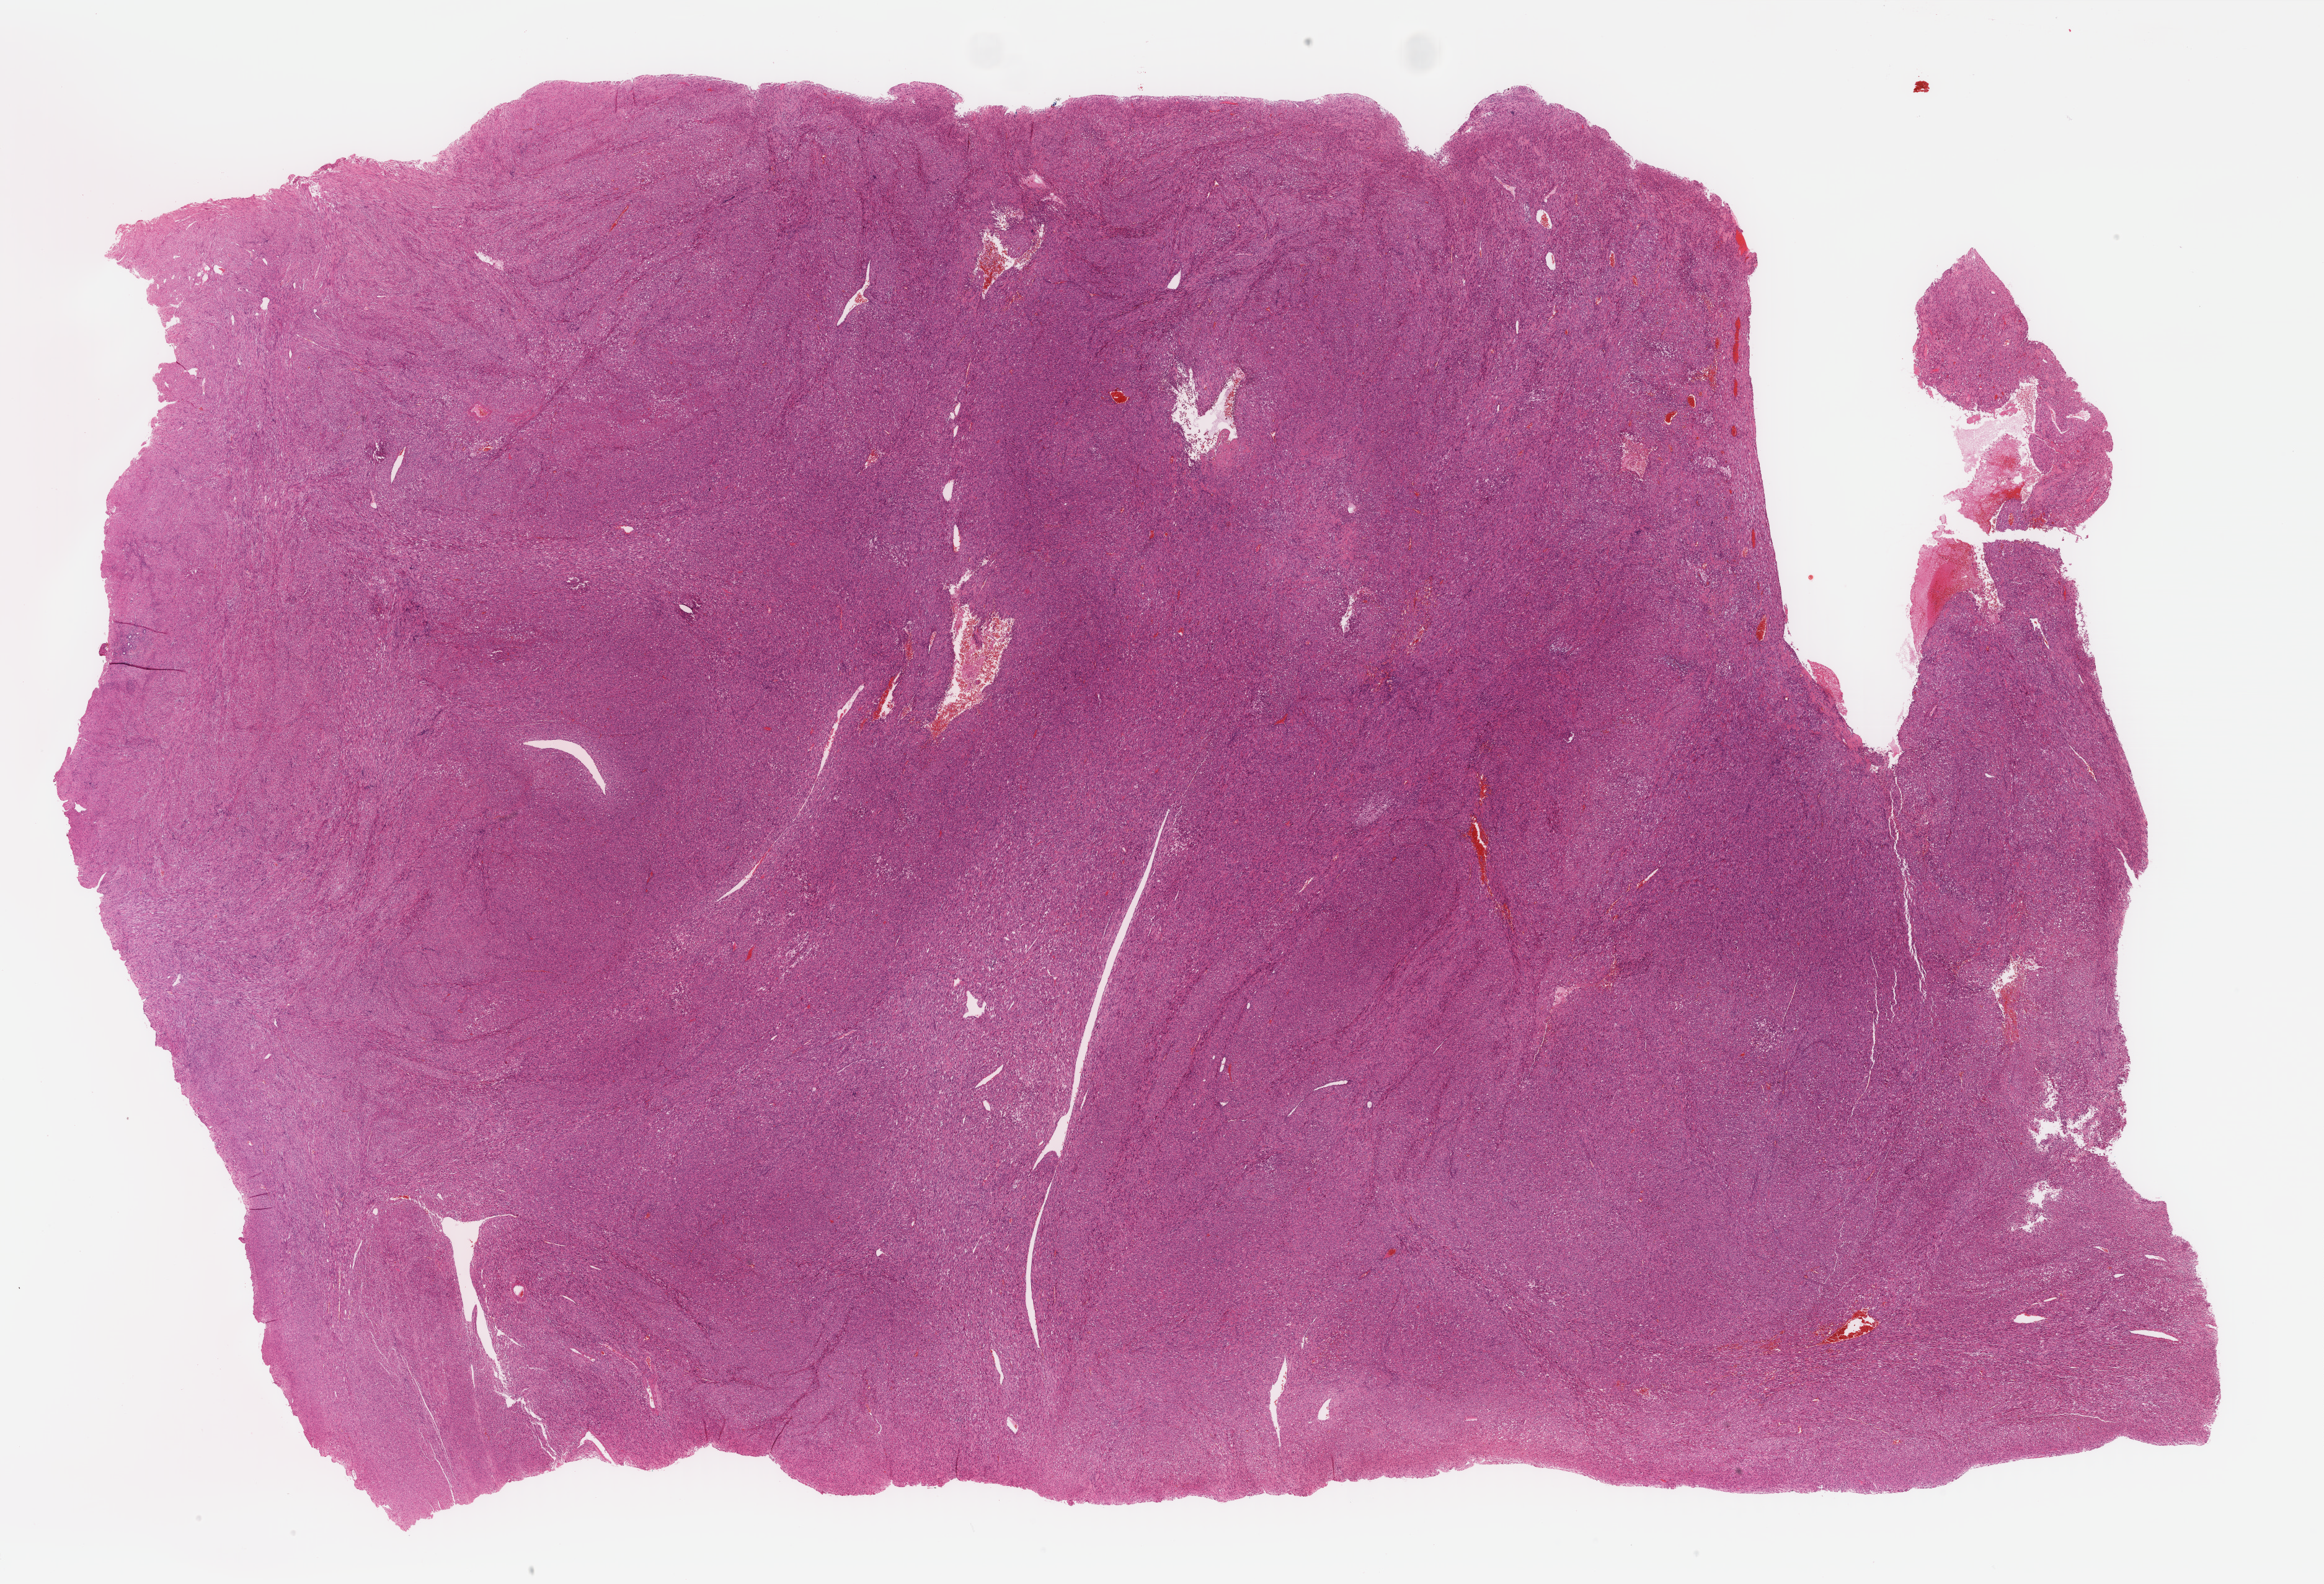
H&E-stained whole-slide image, a low-resolution overview of the entire scanned area, about 29.7 x 20.3 mm (slide scanned at 40x), FFPE section, primary tumour sample from the uterus. Female, age 59 years at initial diagnosis.
Histologic diagnosis: Leiomyosarcoma, NOS.